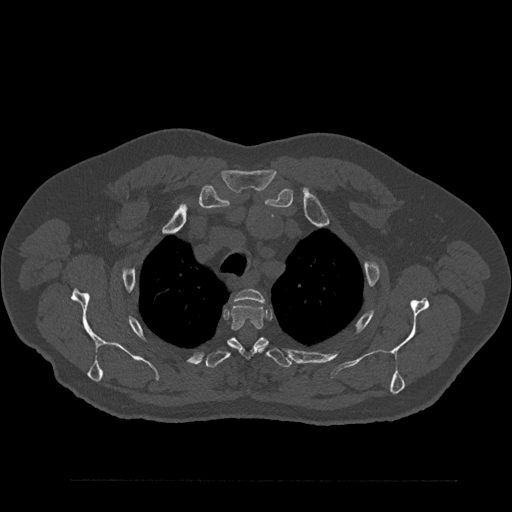
CT including the spine, one axial slice; slice 672 of 797 in the series (ordered by position); reconstruction kernel Br40s/3; 120 kVp; bone window (W 1800 / L 400 HU); 0.5 mm slice thickness; 512 × 512 image matrix, field of view 430 × 430 mm. Patient: male, 61 years. From the clinical record (not read from this slice): primary cancer: prostate.
Outlined on this slice (semi-automatic segmentation, software-assisted and operator-edited):
- T2 vertebra: bounding box (x1, y1, x2, y2) in pixels: (235, 289, 265, 303)
- T3 vertebra: (231, 303, 264, 352)
- T4 vertebra: (206, 337, 291, 368)